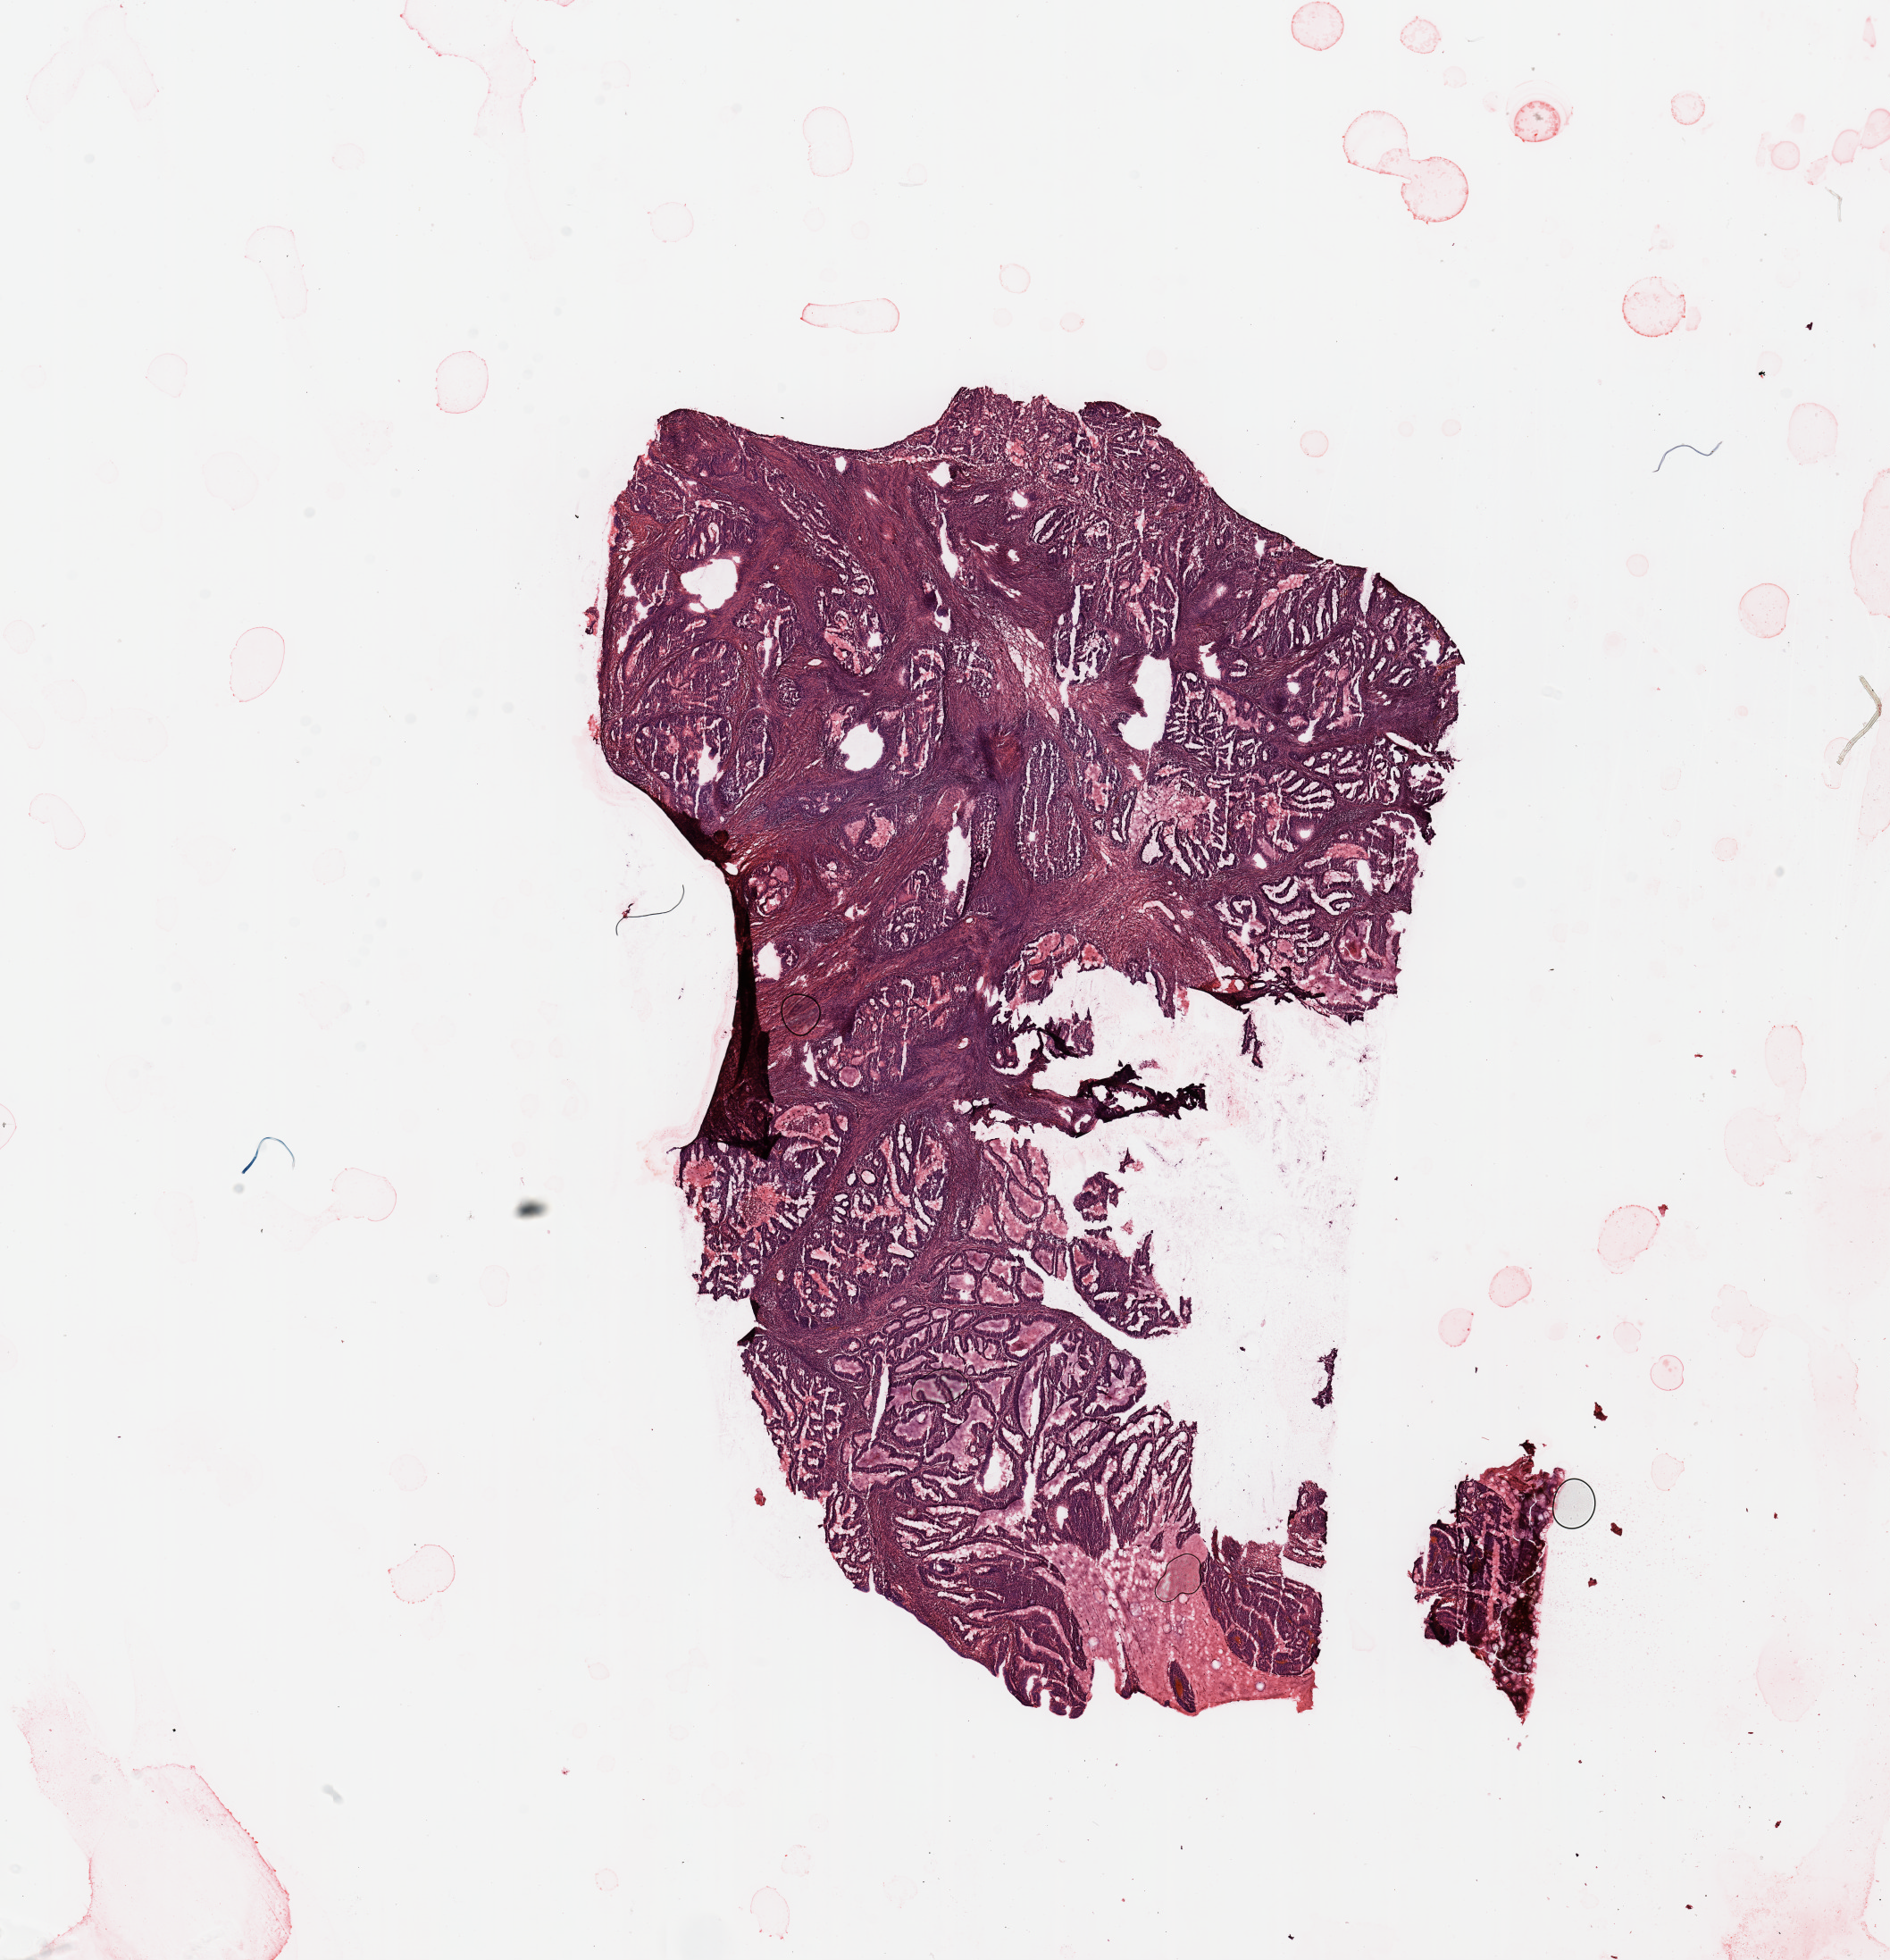
H&E-stained whole-slide image — shown as a low-resolution overview of the whole scanned area (about 16.7 x 17.4 mm). Tumour tissue sample, uterus. 65-year-old female patient. Histologic grade: G2 (moderately differentiated).
• AJCC pathologic stage: I
• histologic diagnosis: Endometrioid adenocarcinoma, NOS